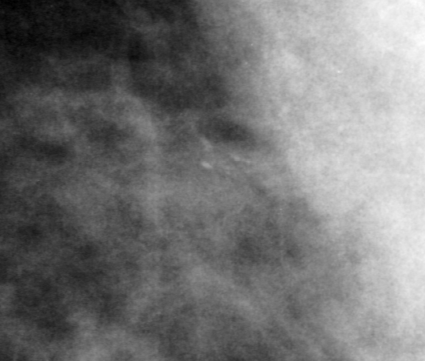
Cropped region of a digitized screen-film mammogram centred on a radiologist-marked abnormality; left breast; MLO view; BI-RADS breast density category 4 (scale 1–4).
Finding: calcifications, morphology pleomorphic, distribution clustered; BI-RADS assessment category 3; subtlety rating 2 on a 1 (subtle) to 5 (obvious) scale; pathology result (as recorded, not read from the image): benign.